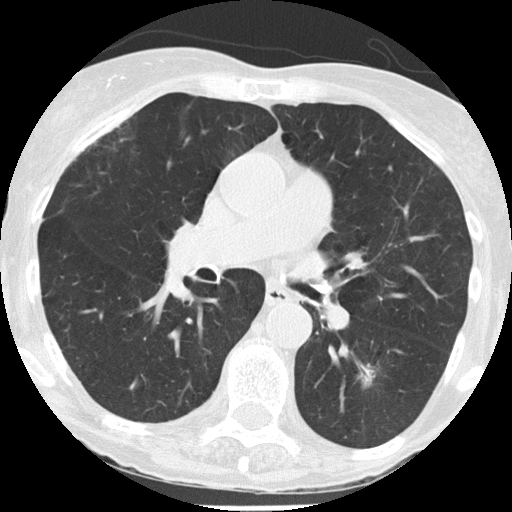
Axial slice from a low-dose chest CT screening exam; third annual screen; lung window (W 1500 / L -600 HU); 120 kVp; slice 74 of 146 in the series; 512 × 512 image matrix. Female, age 68 years at enrolment. Former smoker at enrolment.
Expert-annotated lung lesion, box from (x=338, y=350) to (x=397, y=402) px. Screening reader's record for this exam (one nodule recorded; not confirmed to be the boxed lesion): non-calcified nodule or mass ≥4 mm, left lower lobe, 11 × 9 mm, spiculated (stellate) margins, soft tissue attenuation, pre-existing on the prior screen: yes; interval growth: yes. Official screen result: positive, other. Participant outcome: lung cancer diagnosed 164 days after this screen — non-small cell carcinoma, left lower lobe, poorly differentiated (G3), stage IA (AJCC 6th edition), 10 mm at pathology.